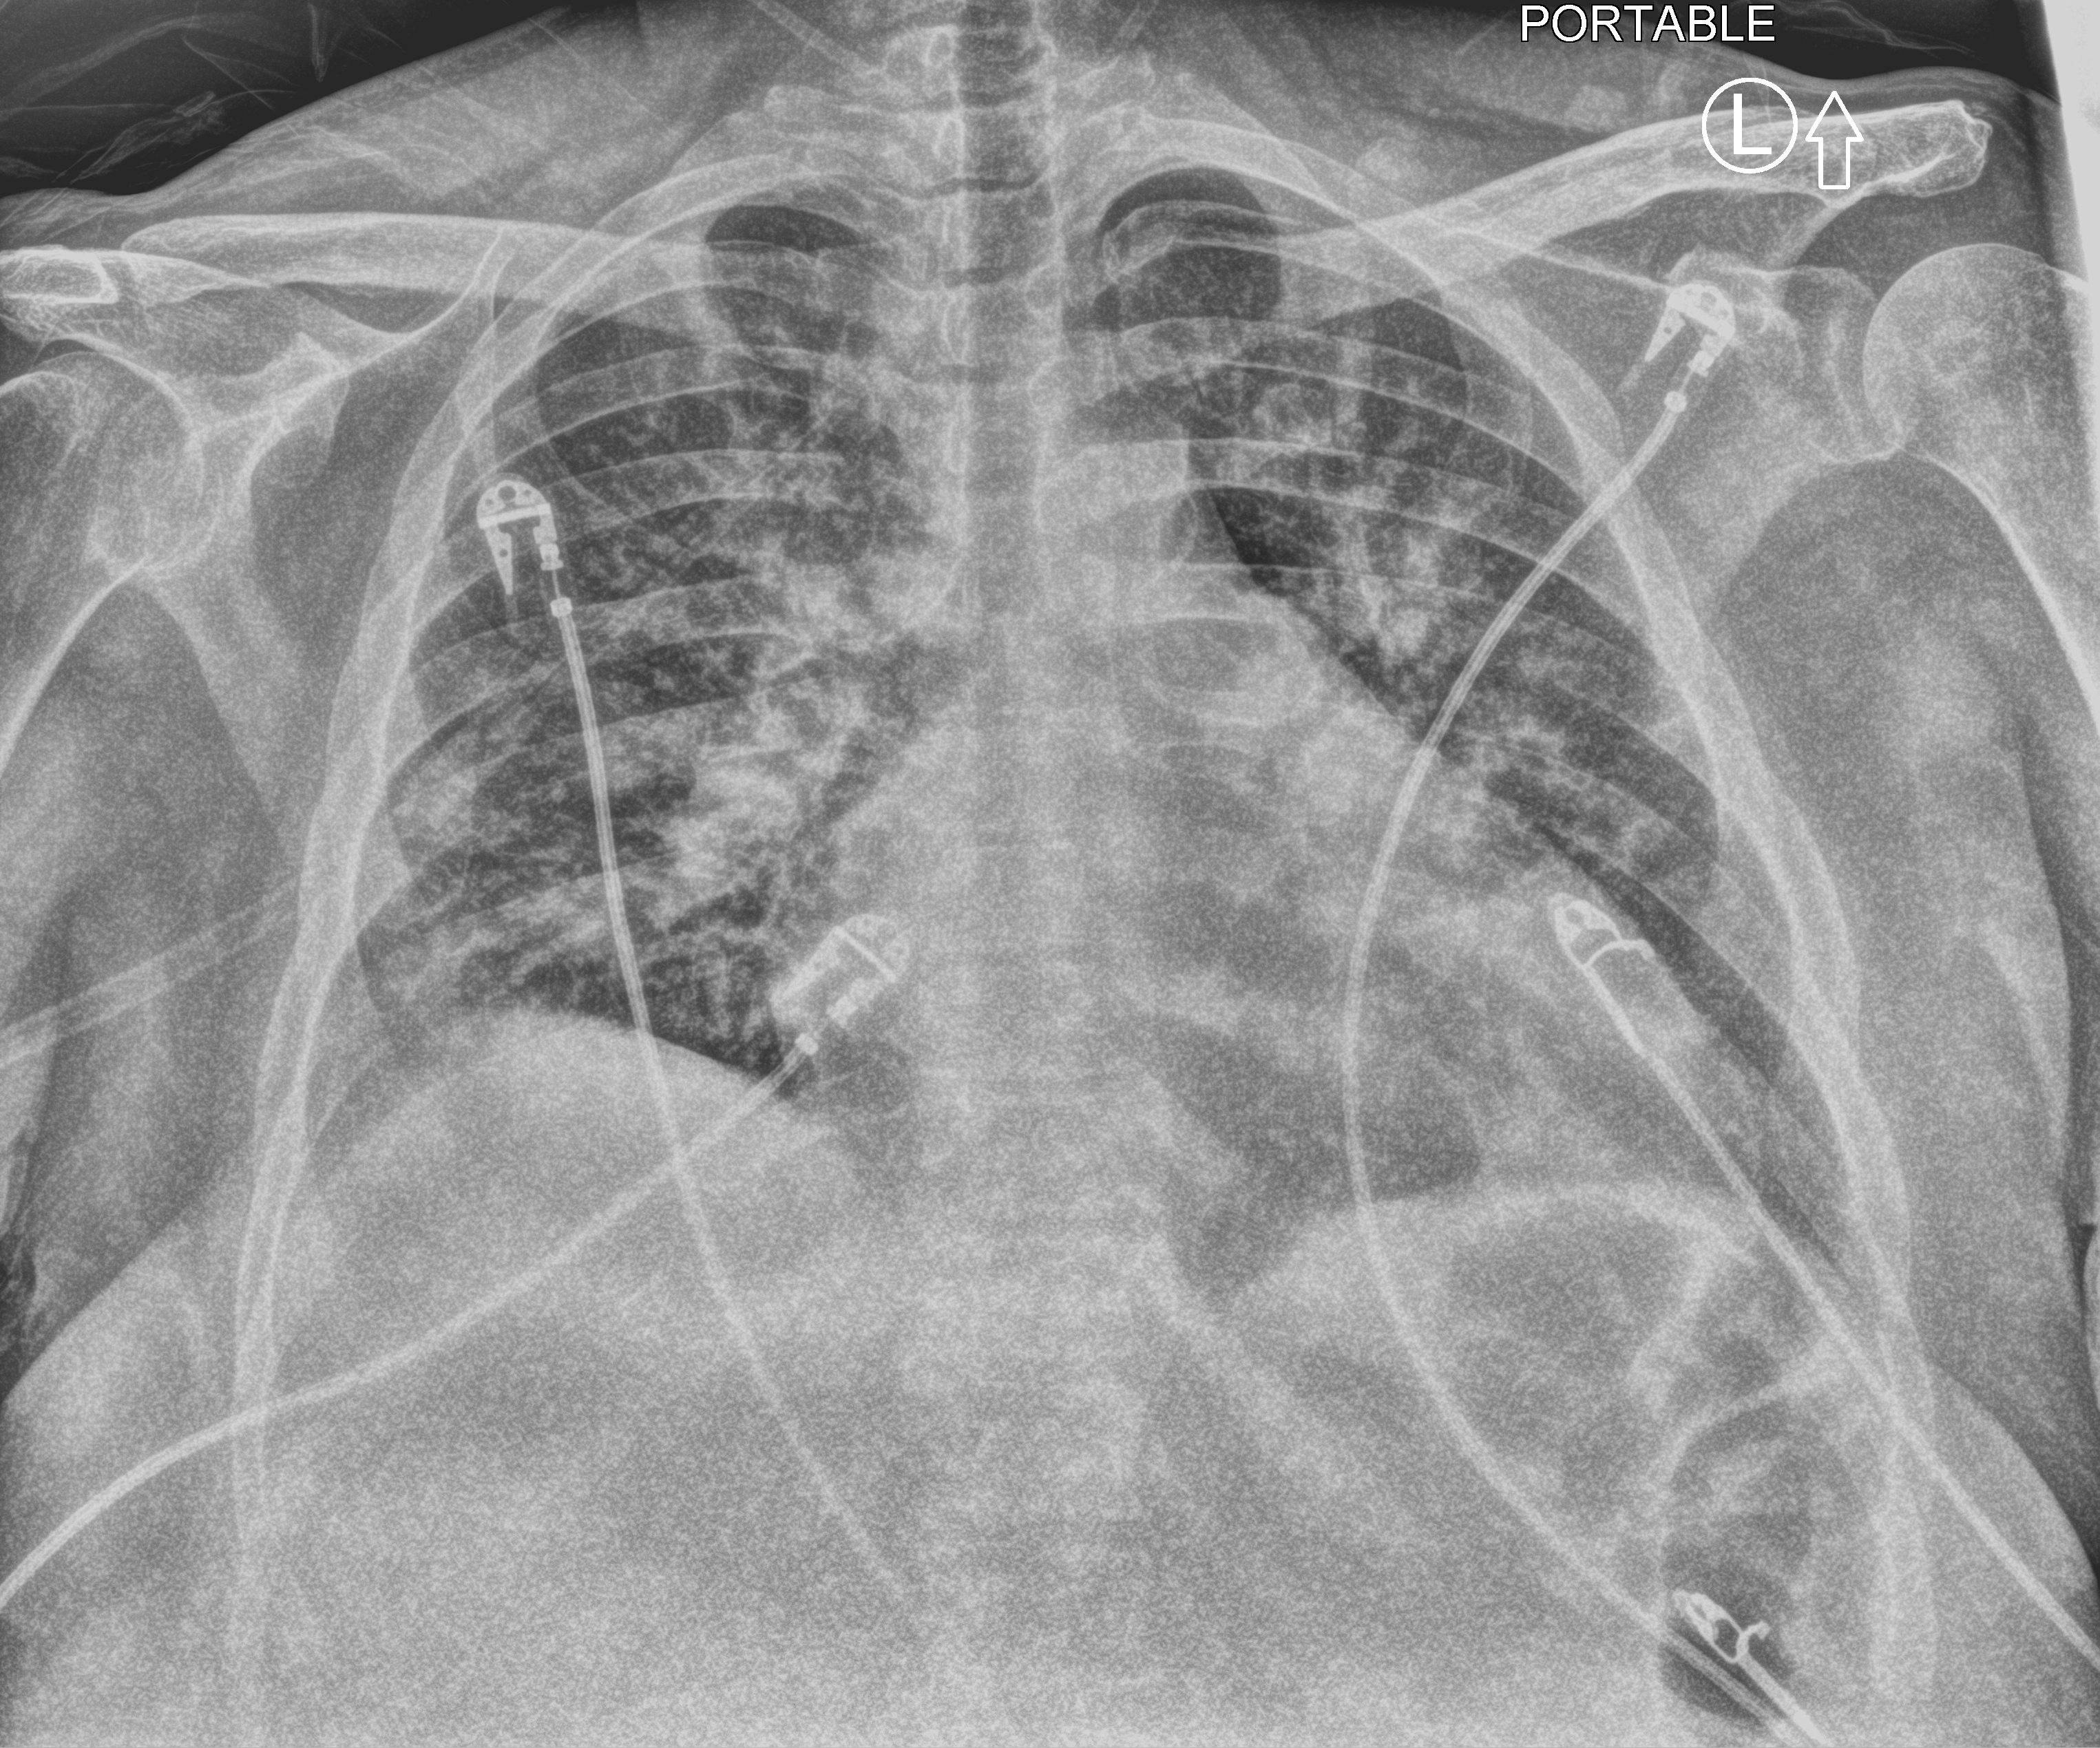
Bedside chest radiograph (computed radiography); anteroposterior (AP) projection. Patient hospitalised with COVID-19; female, aged 60–74 years.
From the hospital-stay record, not from the radiograph (when in the stay this image was taken is not recorded): smoking status (admission record): never; mechanically ventilated during this hospital stay: no; other chronic lung disease (admission record): yes.